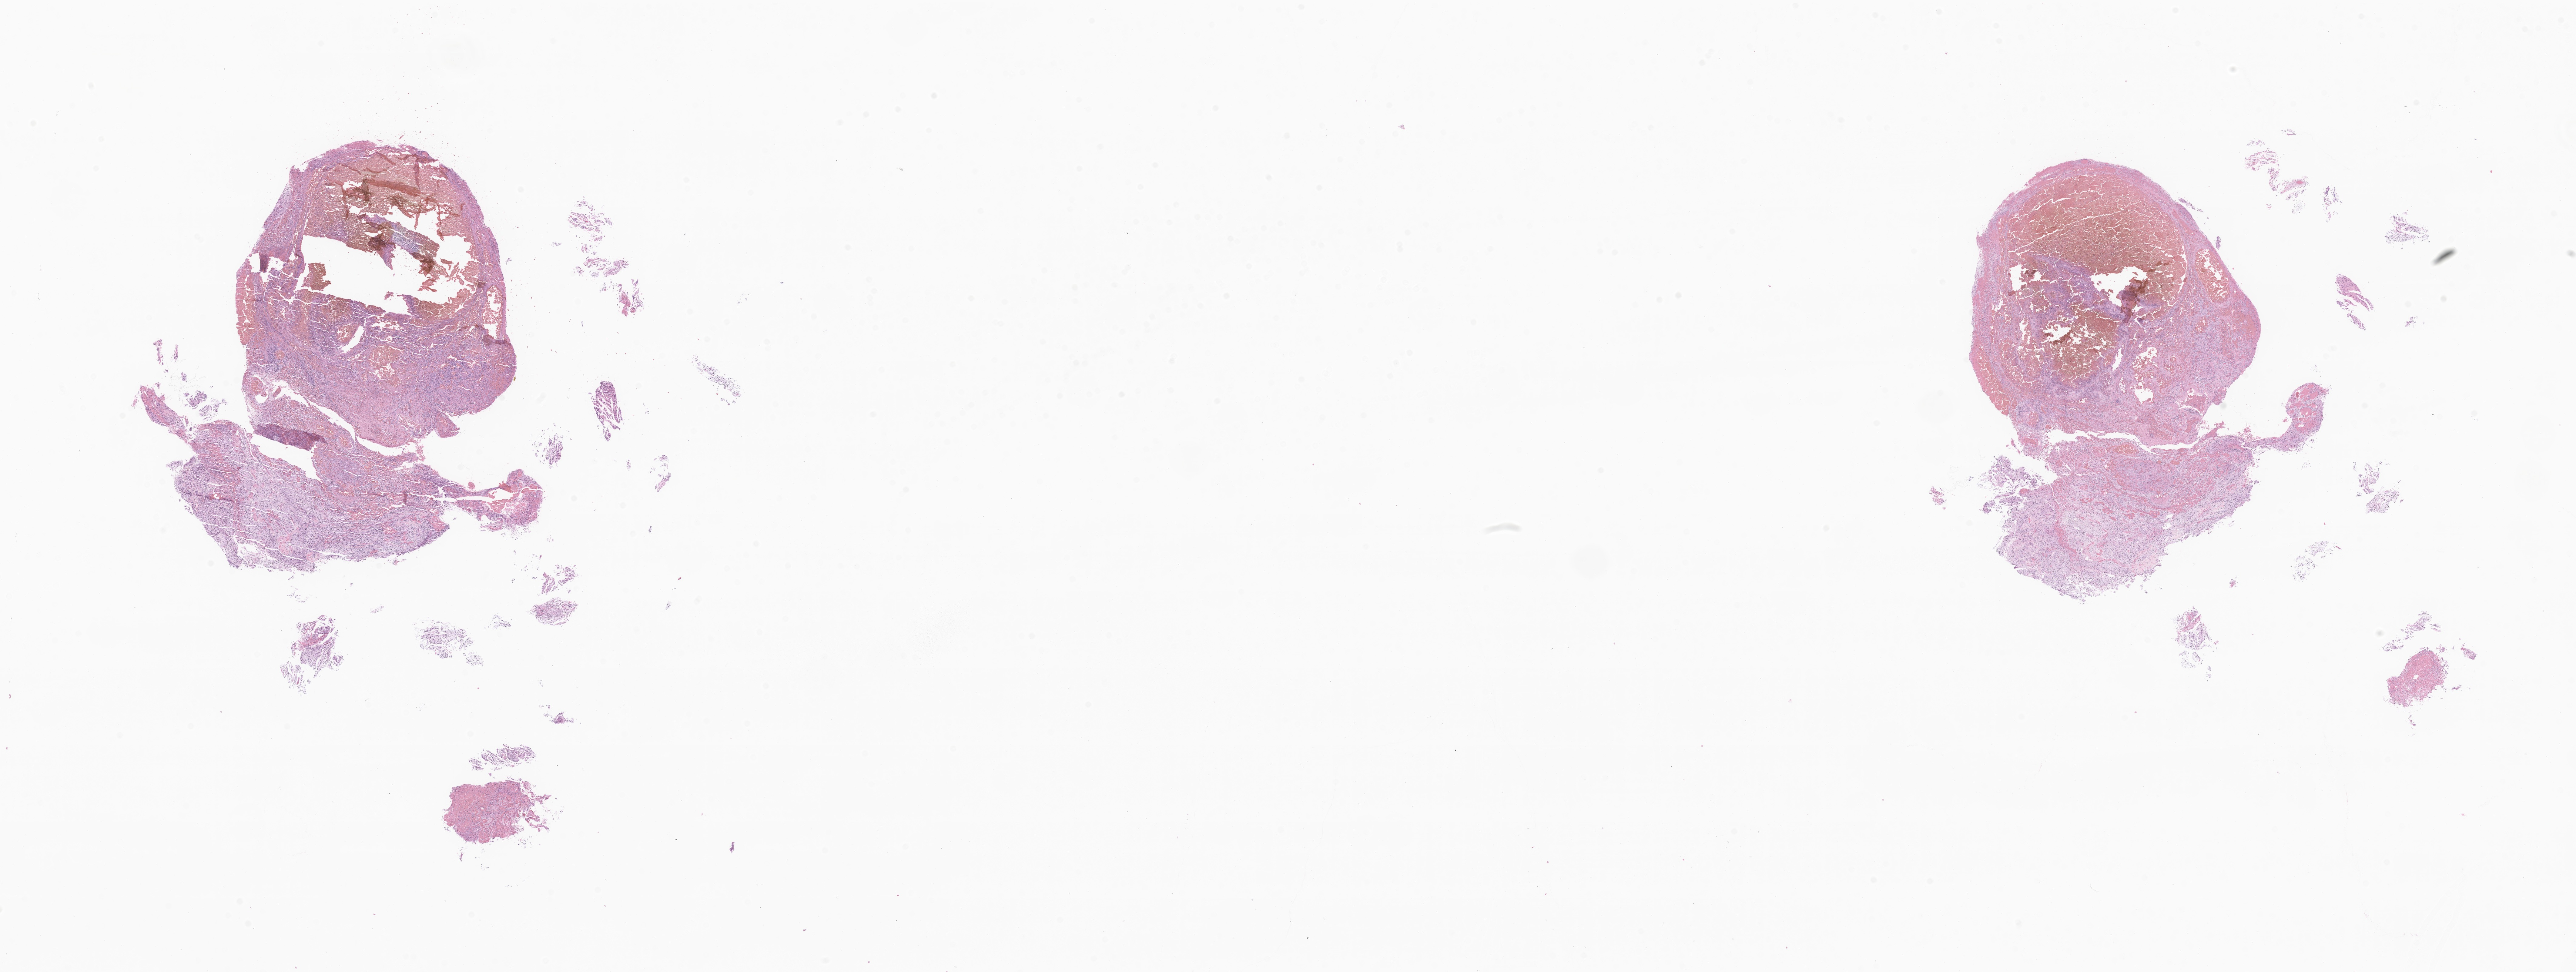
Whole-slide image, hematoxylin and eosin (H&E) stain of tumor tissue from the brain, low-resolution overview of the scanned area, about 35.8 x 13.5 mm; formalin-fixed paraffin-embedded section. Patient male; age 157 months (13 years 1 month).
Diagnosis (ICD-O-3 morphology term): Neoplasm, uncertain whether benign or malignant.